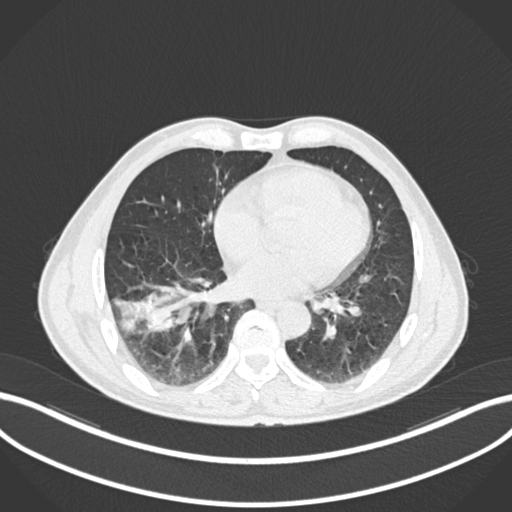
Chest CT, one axial slice. Slice 72 of 208 in the series (ordered by position). 120 kVp. Lung window (W 1500 / L -600 HU). 1 mm slice thickness. 512 × 512 image matrix, field of view 400 × 400 mm. Male patient, age 58 years. From the clinical record (not read from this slice): clinical TNM (as recorded): T3 N0 M0.
Annotated regions visible in this slice (bounding box drawn by a radiologist):
- lung tumour (recorded histology: squamous cell carcinoma): bounding box <113,288,193,336> (left, top, right, bottom; pixels)